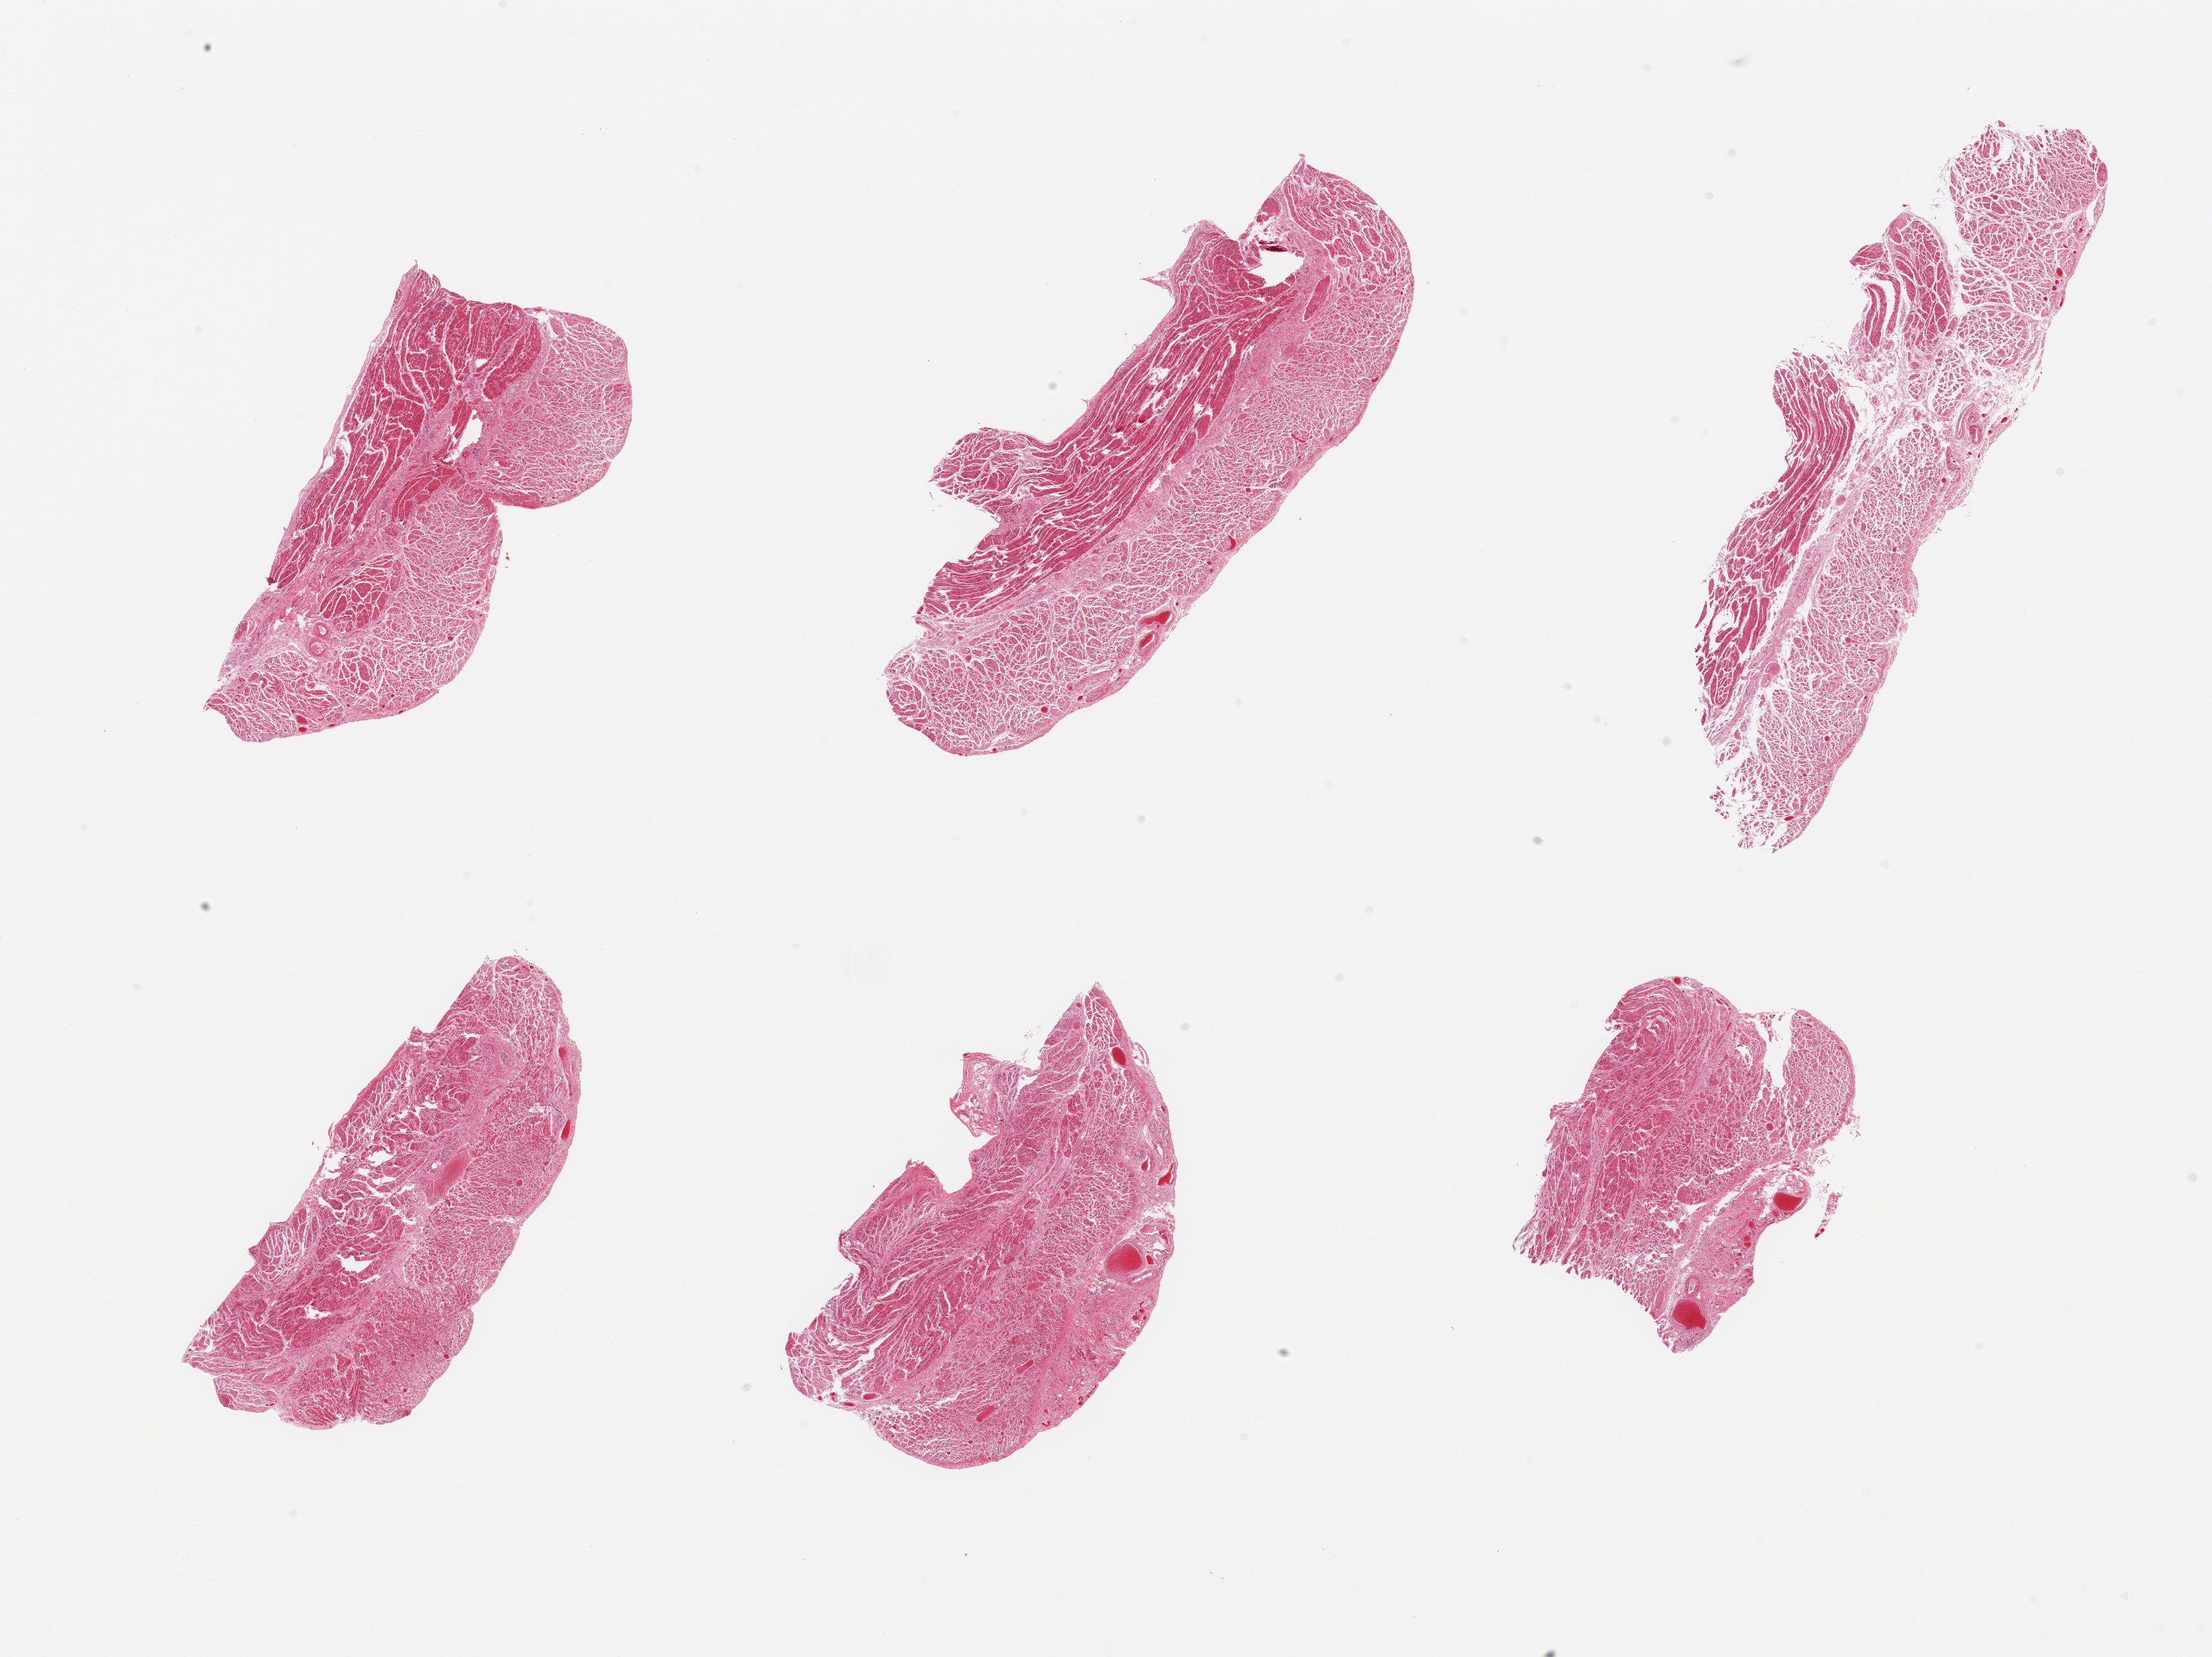
Whole-slide image, H&E stain — a low-resolution overview of the entire scanned area, about 25.6 x 19.2 mm. PAXgene-fixed paraffin-embedded (PFPE) section. Sampled site (target tissue): gastroesophageal junction. Tissue donor sample.
Pathologist's review note for this sample: 6 pieces, confirmed target muscularis.